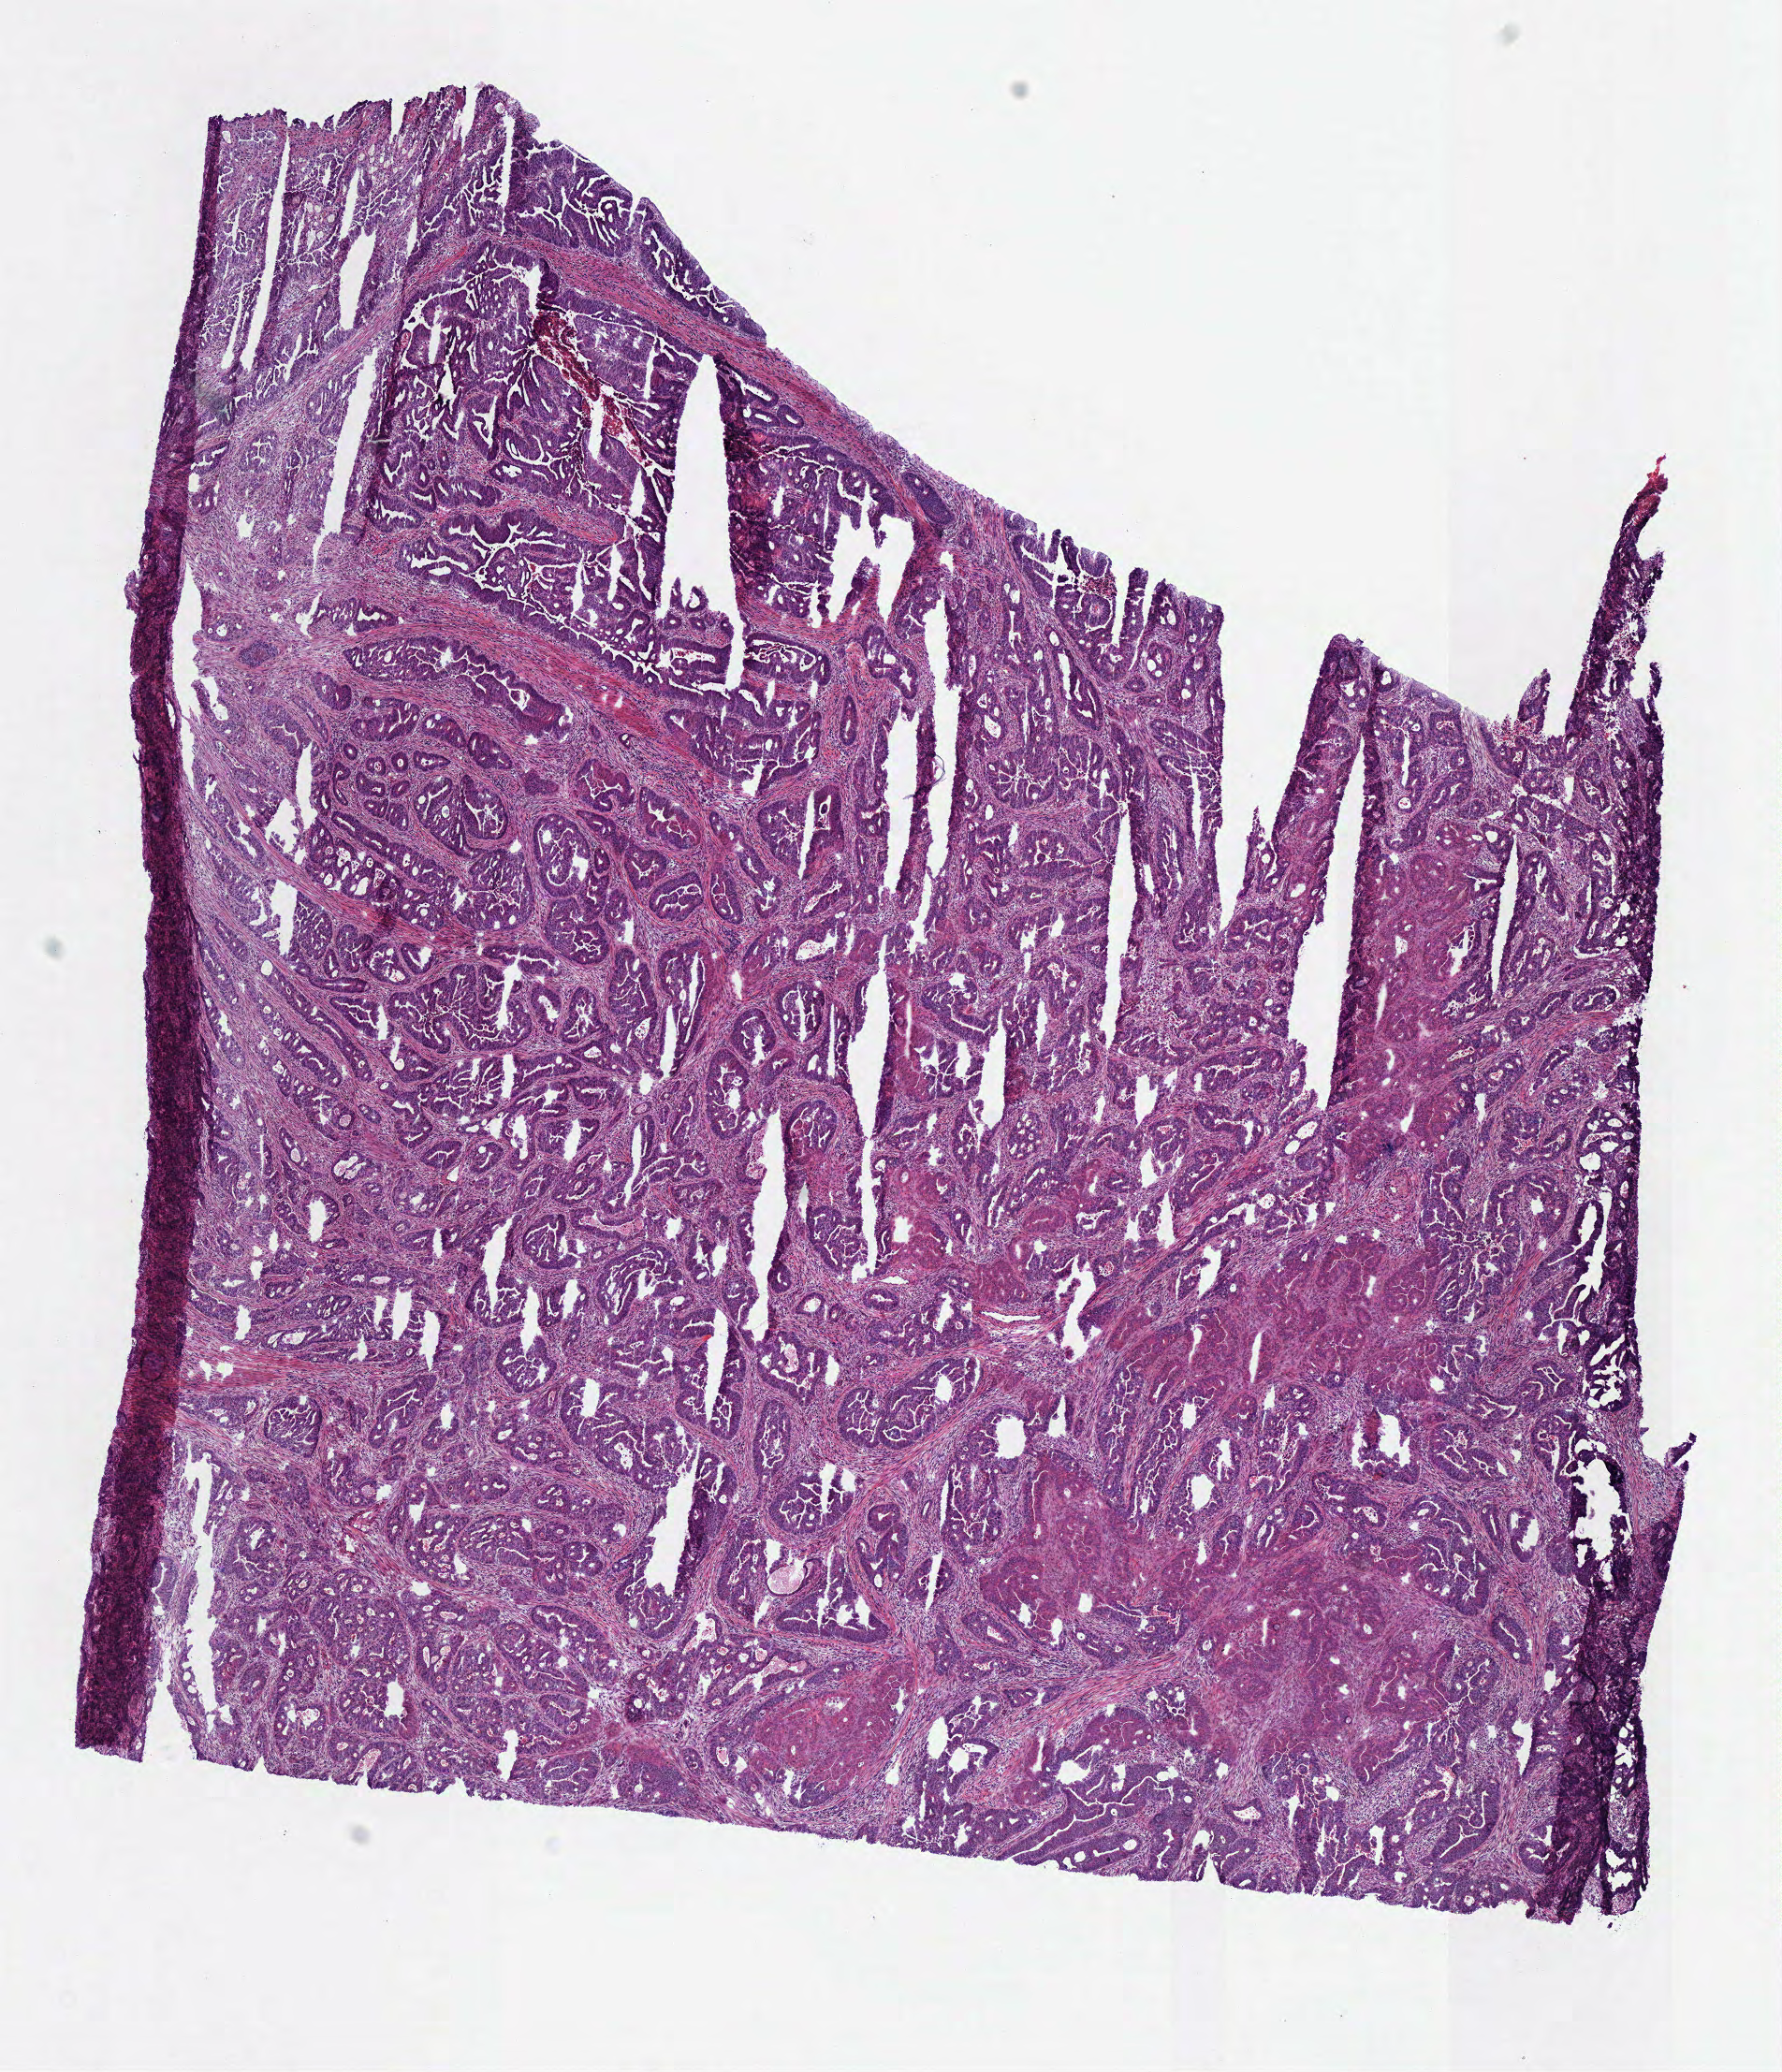
Whole-slide histology image, H&E-stained — shown as a low-resolution overview of the whole scanned area (about 7.5 x 8.7 mm, slide scanned at 40x). Frozen section. Primary tumour sample from the colon. Patient: male, age at initial diagnosis 57 years.
Histologic diagnosis: Adenocarcinoma, NOS (sigmoid colon).